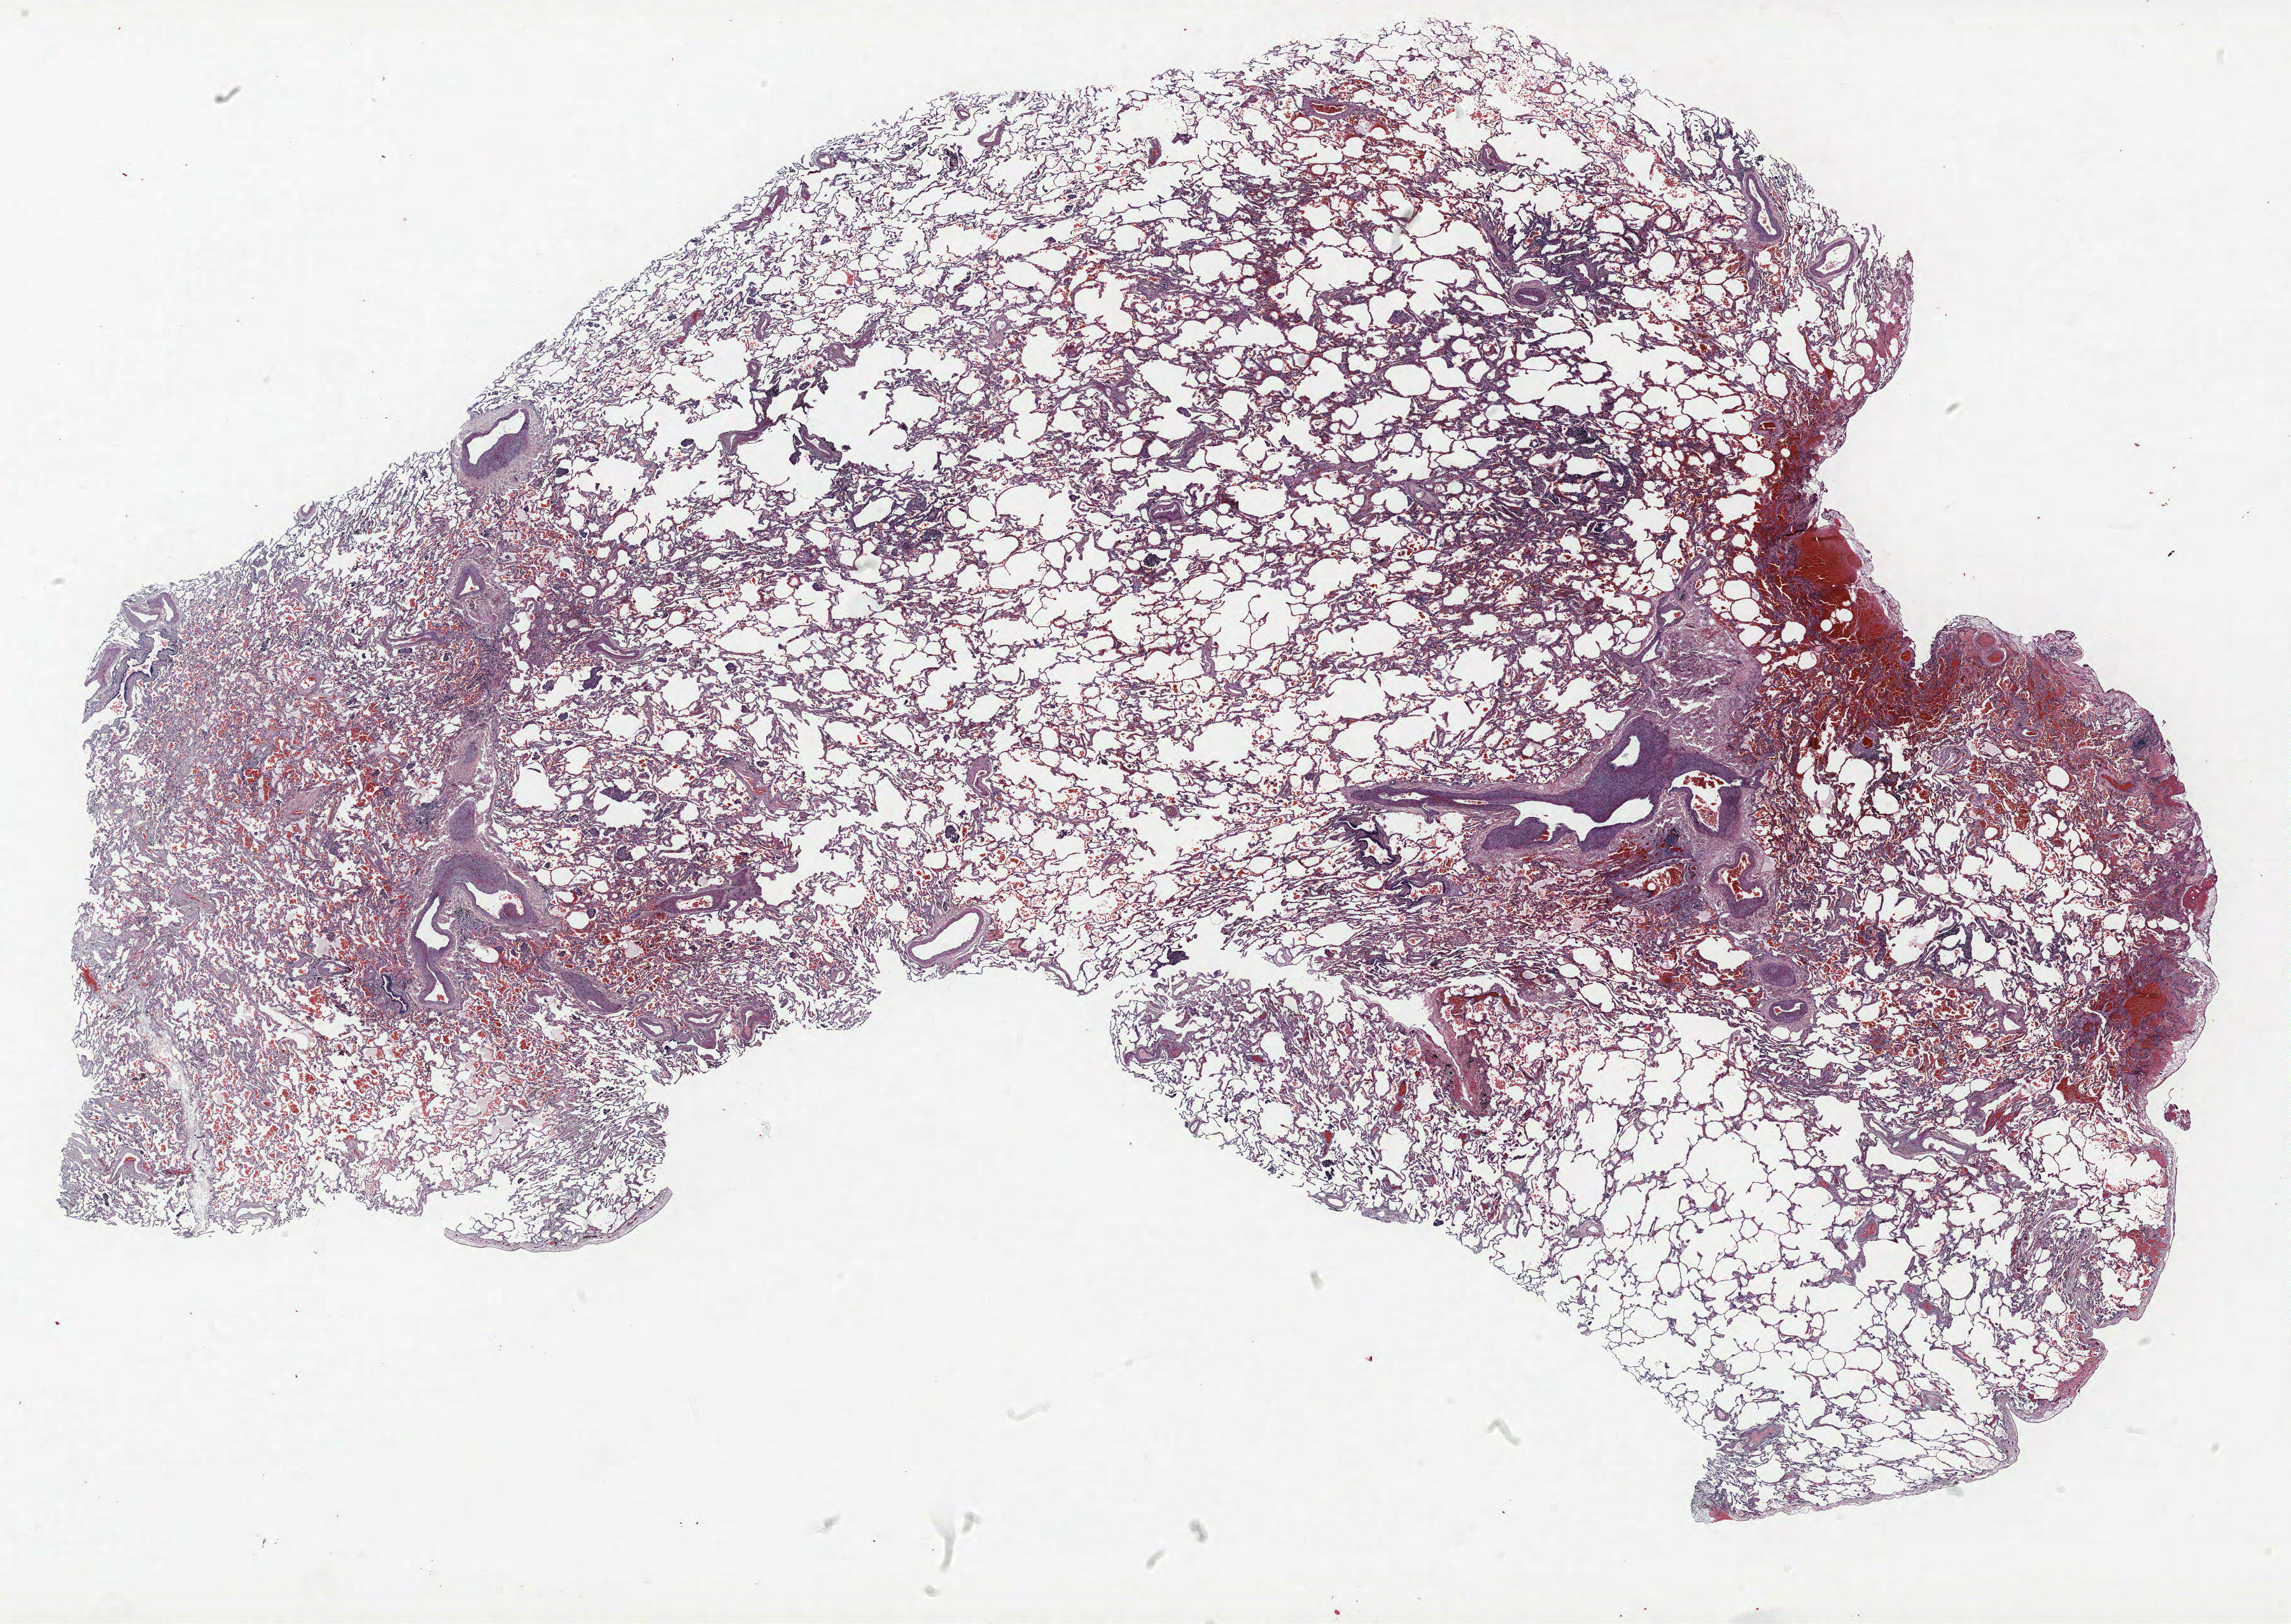
H&E whole-slide image — shown as a low-resolution overview of the whole scanned area (about 28.8 x 20.4 mm). Formalin-fixed paraffin-embedded (FFPE) section. Lung tissue. Male patient, aged 63 at enrolment. Former smoker at enrolment. Grade: moderately differentiated (G2).
Primary tumour location (clinical record): left lower lobe. ICD-O-3 topography: lower lobe of lung (C34.3). Stage (AJCC 6th edition): IA. Tumour size (pathology): 15 mm. Participant's lung-cancer diagnosis: Squamous cell carcinoma, NOS.